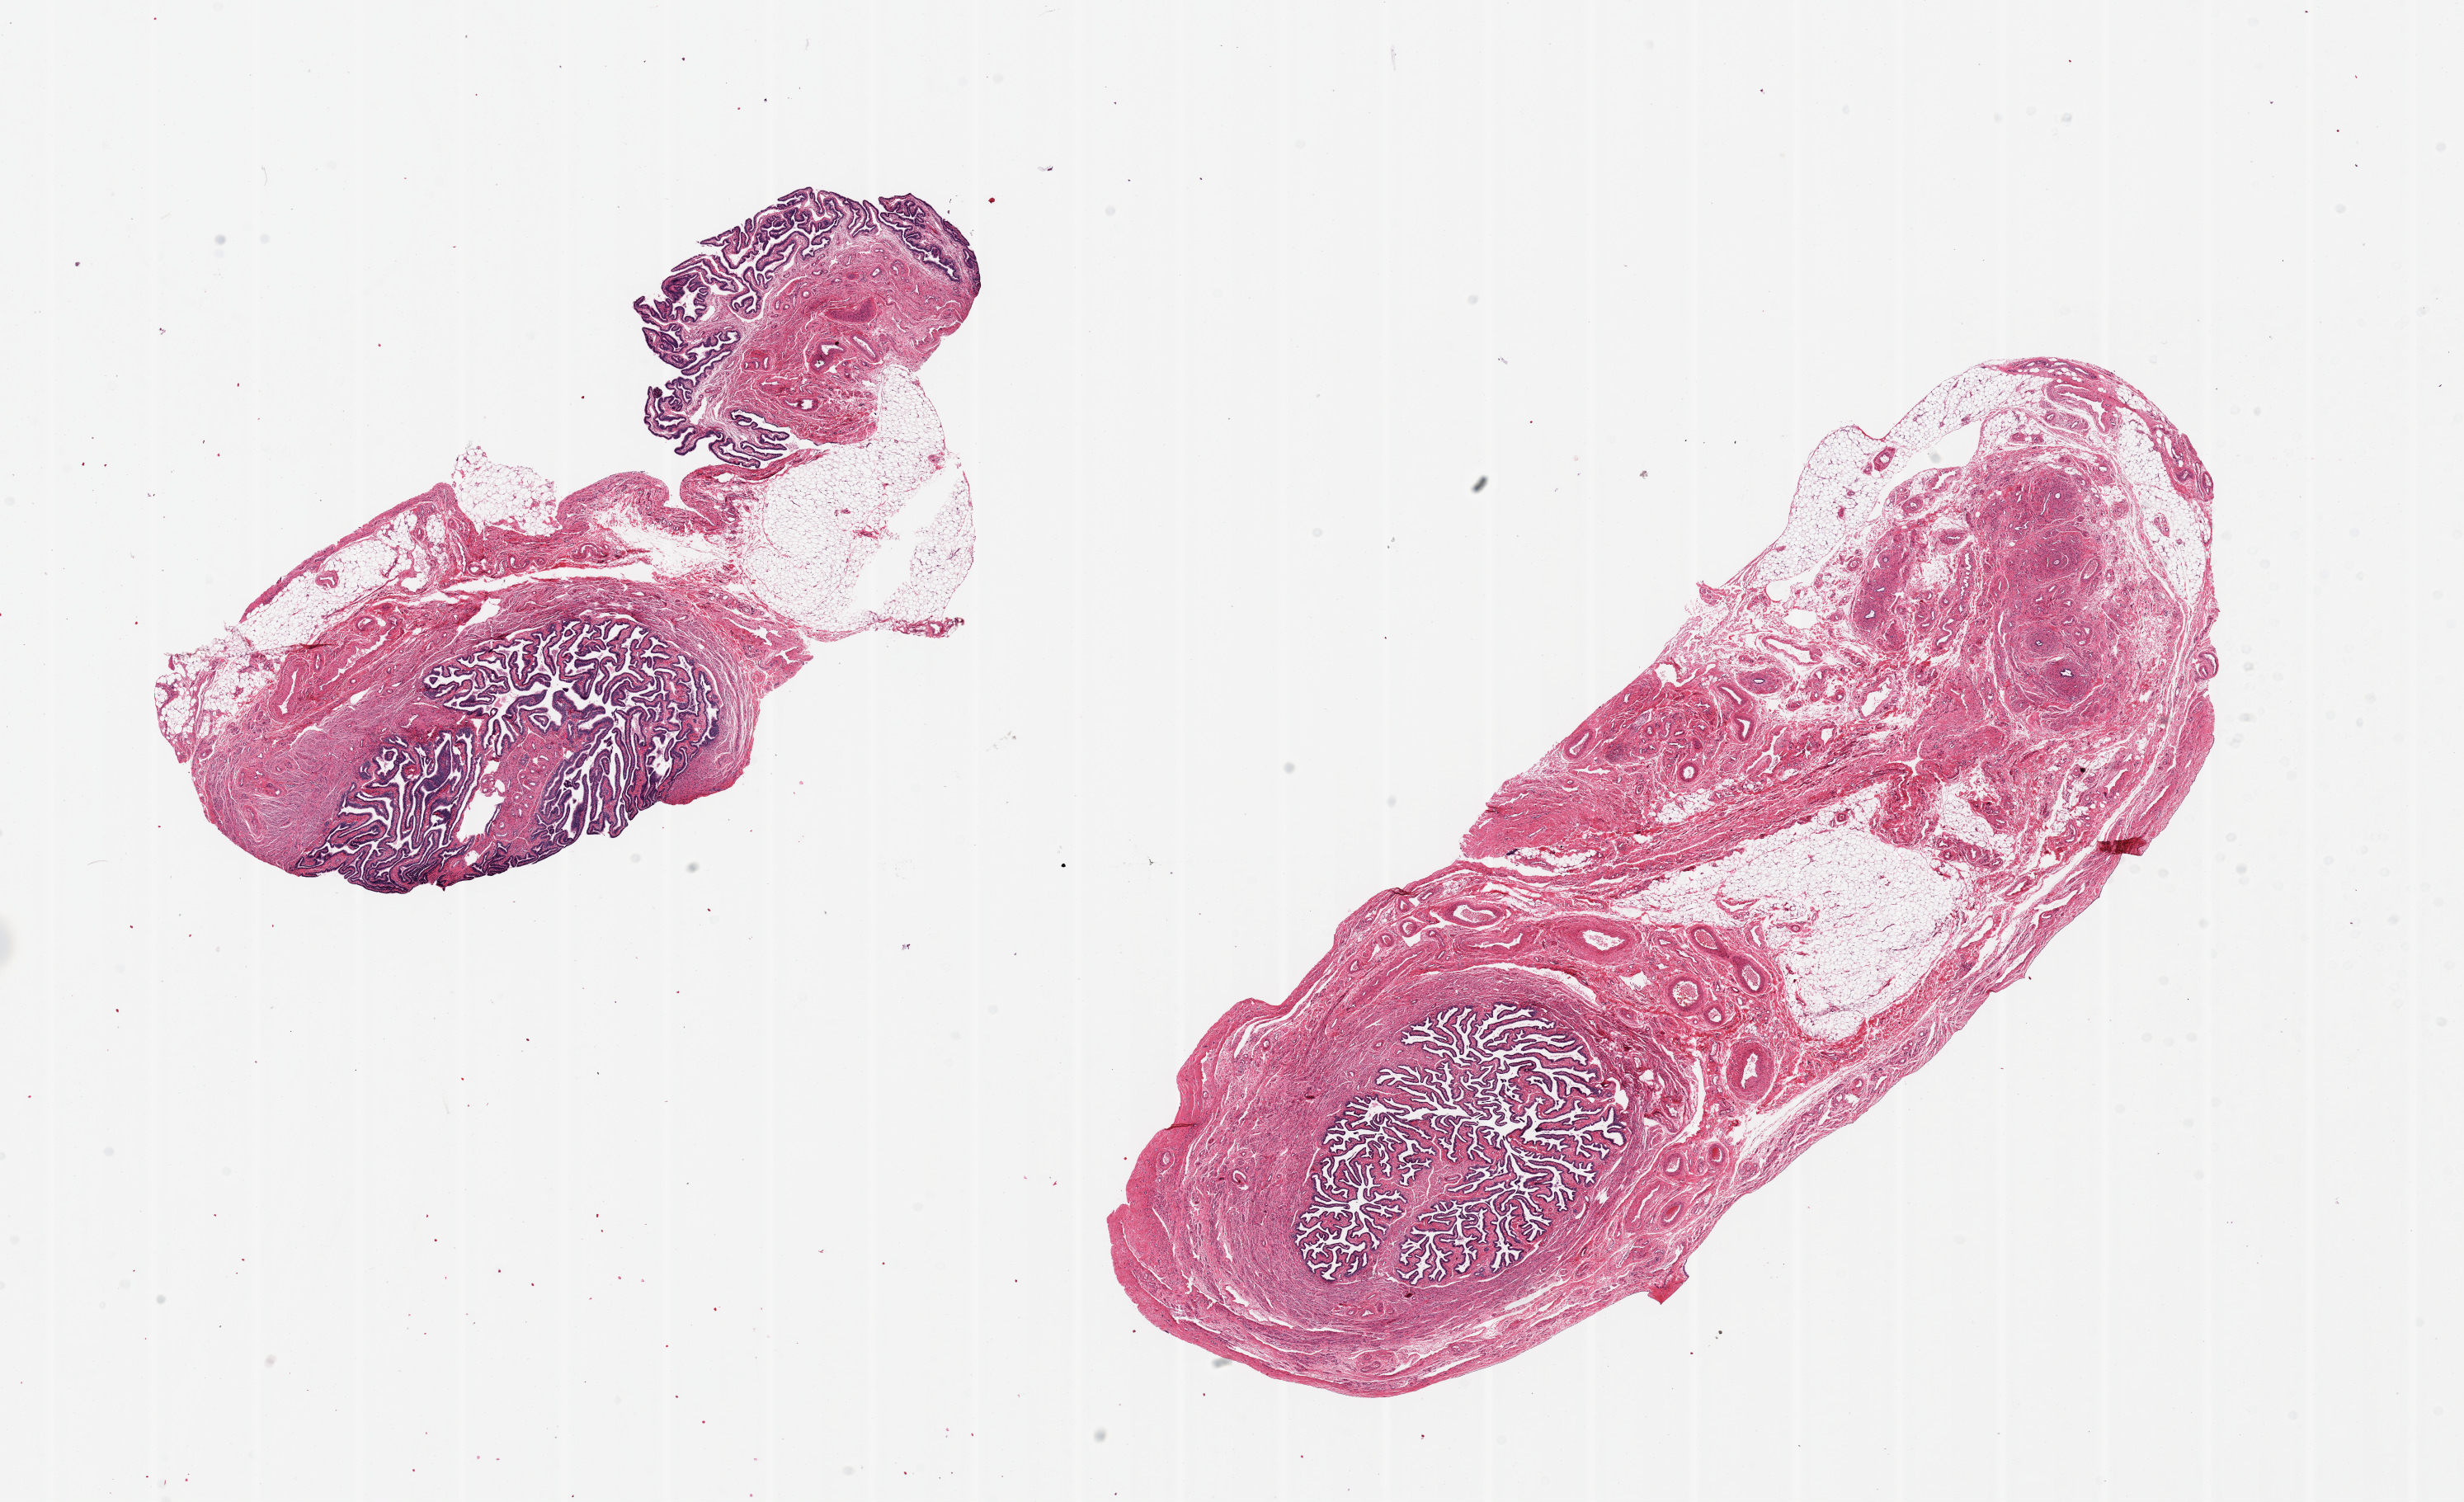
Whole-slide image, H&E stain — shown as a low-resolution overview of the whole scanned area (about 23.6 x 14.4 mm); PAXgene-fixed, paraffin-embedded tissue; section of fallopian tube (target tissue); tissue donor sample. Donor sex: female.
Reviewer comment on this tissue sample: 2 pieces 13x4 & 9x4 mm; 1 piece has 60% fibrofatty vascularized stroma; smaller piece has 30% adipose.